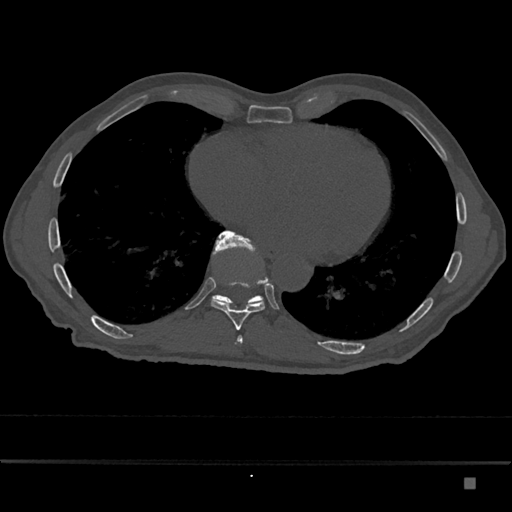
CT including the spine, one axial slice. Slice 786 of 797 in the series (ordered by position). Reconstruction kernel Br40s/3. 120 kVp. Bone window (W 1800 / L 400 HU). 0.5 mm slice thickness. 512 × 512 image matrix, field of view 390 × 390 mm. Patient: male, 72 years. From the clinical record (not read from this slice): primary cancer: prostate.
Structures marked on this image (semi-automatic segmentation, software-assisted and operator-edited):
- T10 vertebra: bounding box [x1, y1, x2, y2] px = [212, 231, 263, 307]
- T9 vertebra: [210, 234, 267, 330]